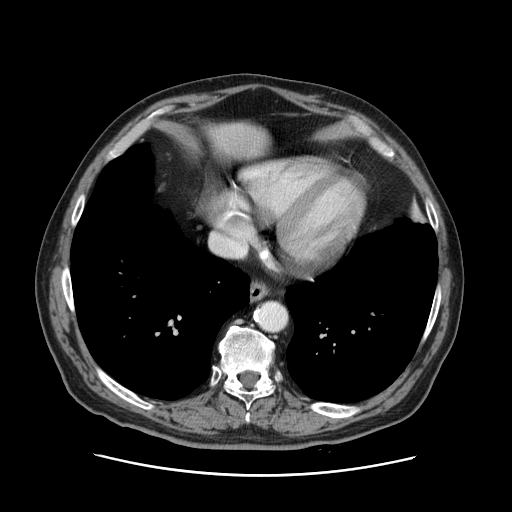
Contrast-enhanced abdominal CT, one axial slice. Slice 124 of 141 in the series (ordered by position). 120 kVp. Intravenous contrast given. Soft-tissue window (W 400 / L 40 HU). 512 × 512 image matrix, field of view 395 × 395 mm. Male patient, age 72 years. Case-level facts recorded for this patient, not image findings: diagnosis: colorectal cancer liver metastases, imaged before liver resection; multiple liver metastases: yes; largest metastasis: 5.4 cm; disease in both lobes: yes.
Outlined on this slice (outlined manually by an expert reader):
- liver: bounding box <205,122,267,158> (left, top, right, bottom; pixels)
- planned liver remnant (the part of the liver to remain after resection): <206,122,267,157>